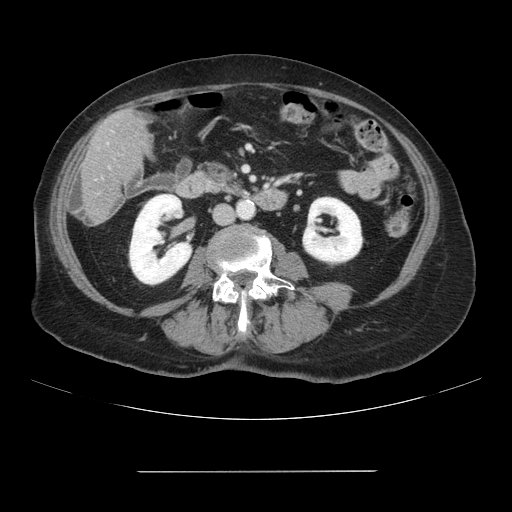
Contrast-enhanced abdominal CT, one axial slice. Slice 14 of 111 in the series (ordered by position). 120 kVp. Intravenous contrast given. Soft-tissue window (W 400 / L 40 HU). 2.5 mm slice thickness. 512 × 512 image matrix, field of view 400 × 400 mm. Female patient, age 74 years. Case-level facts recorded for this patient, not image findings: diagnosis: colorectal cancer liver metastases, imaged before liver resection; multiple liver metastases: yes; largest metastasis: 1.1 cm; disease in both lobes: yes.
Structures marked on this image (manually delineated by an expert):
- liver: bounding box (x1, y1, x2, y2) in pixels: (83, 109, 147, 224)